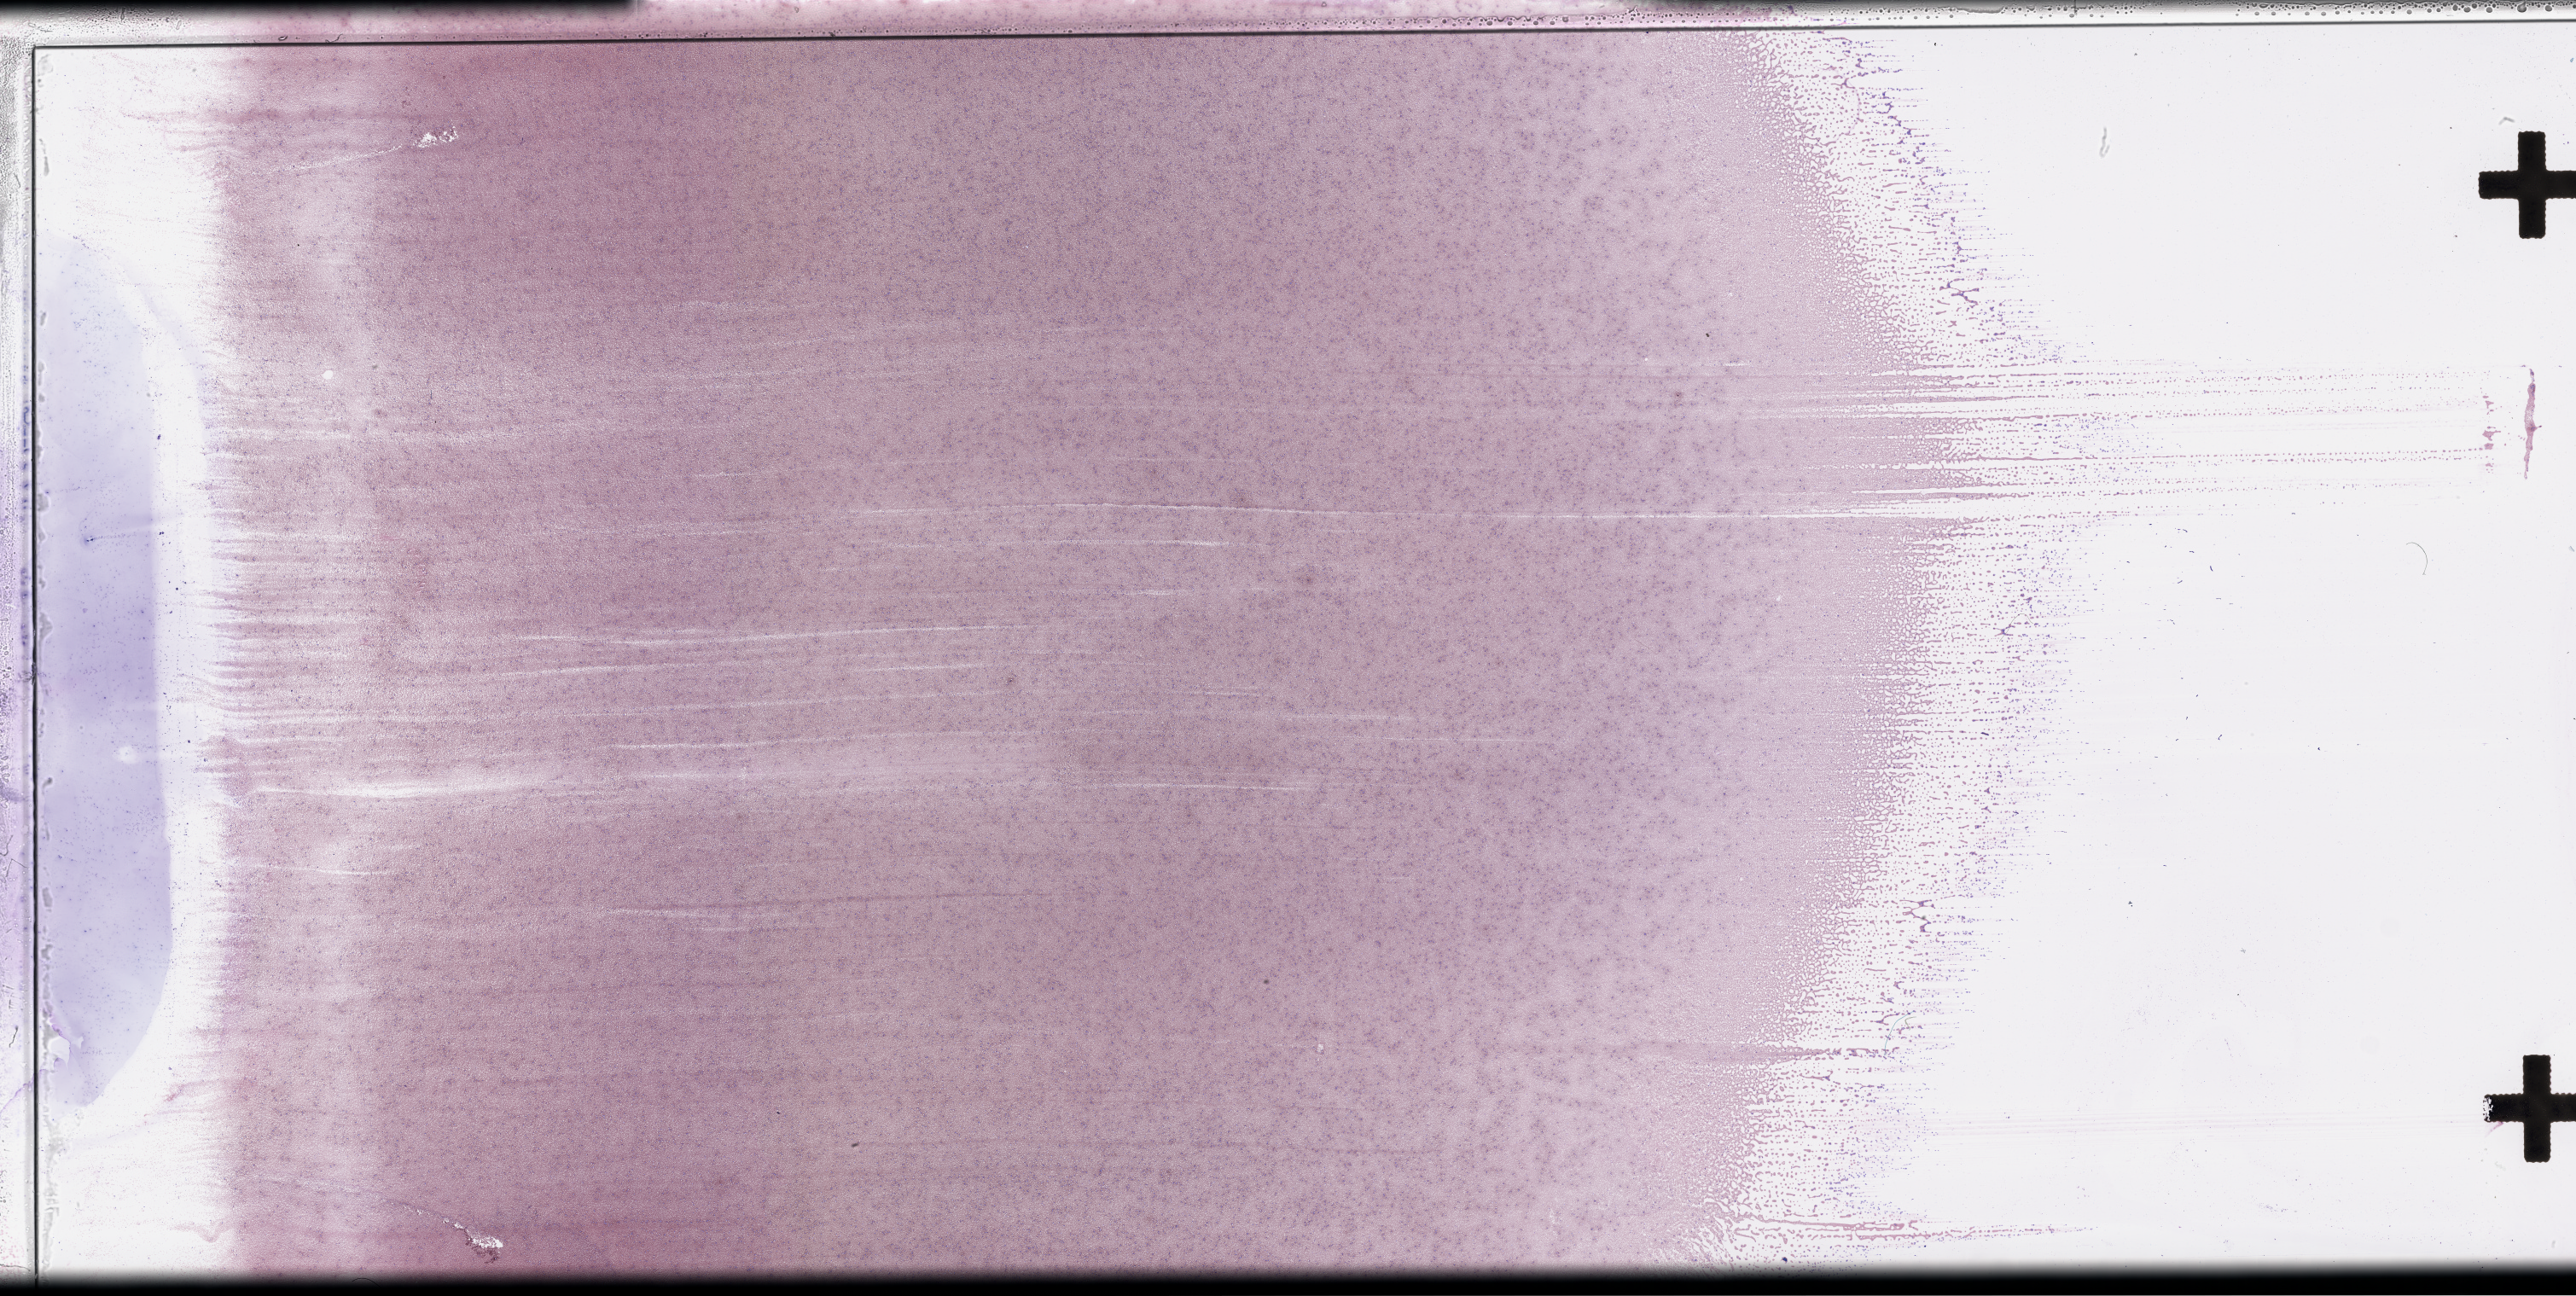
H&E-stained whole-slide image, low-resolution overview of the scanned area, about 48.8 x 24.5 mm (from a 40x scan). Peripheral blood (leukaemic) sample. Patient: female, age 33 years.
Diagnosis: Acute Myeloid Leukemia.